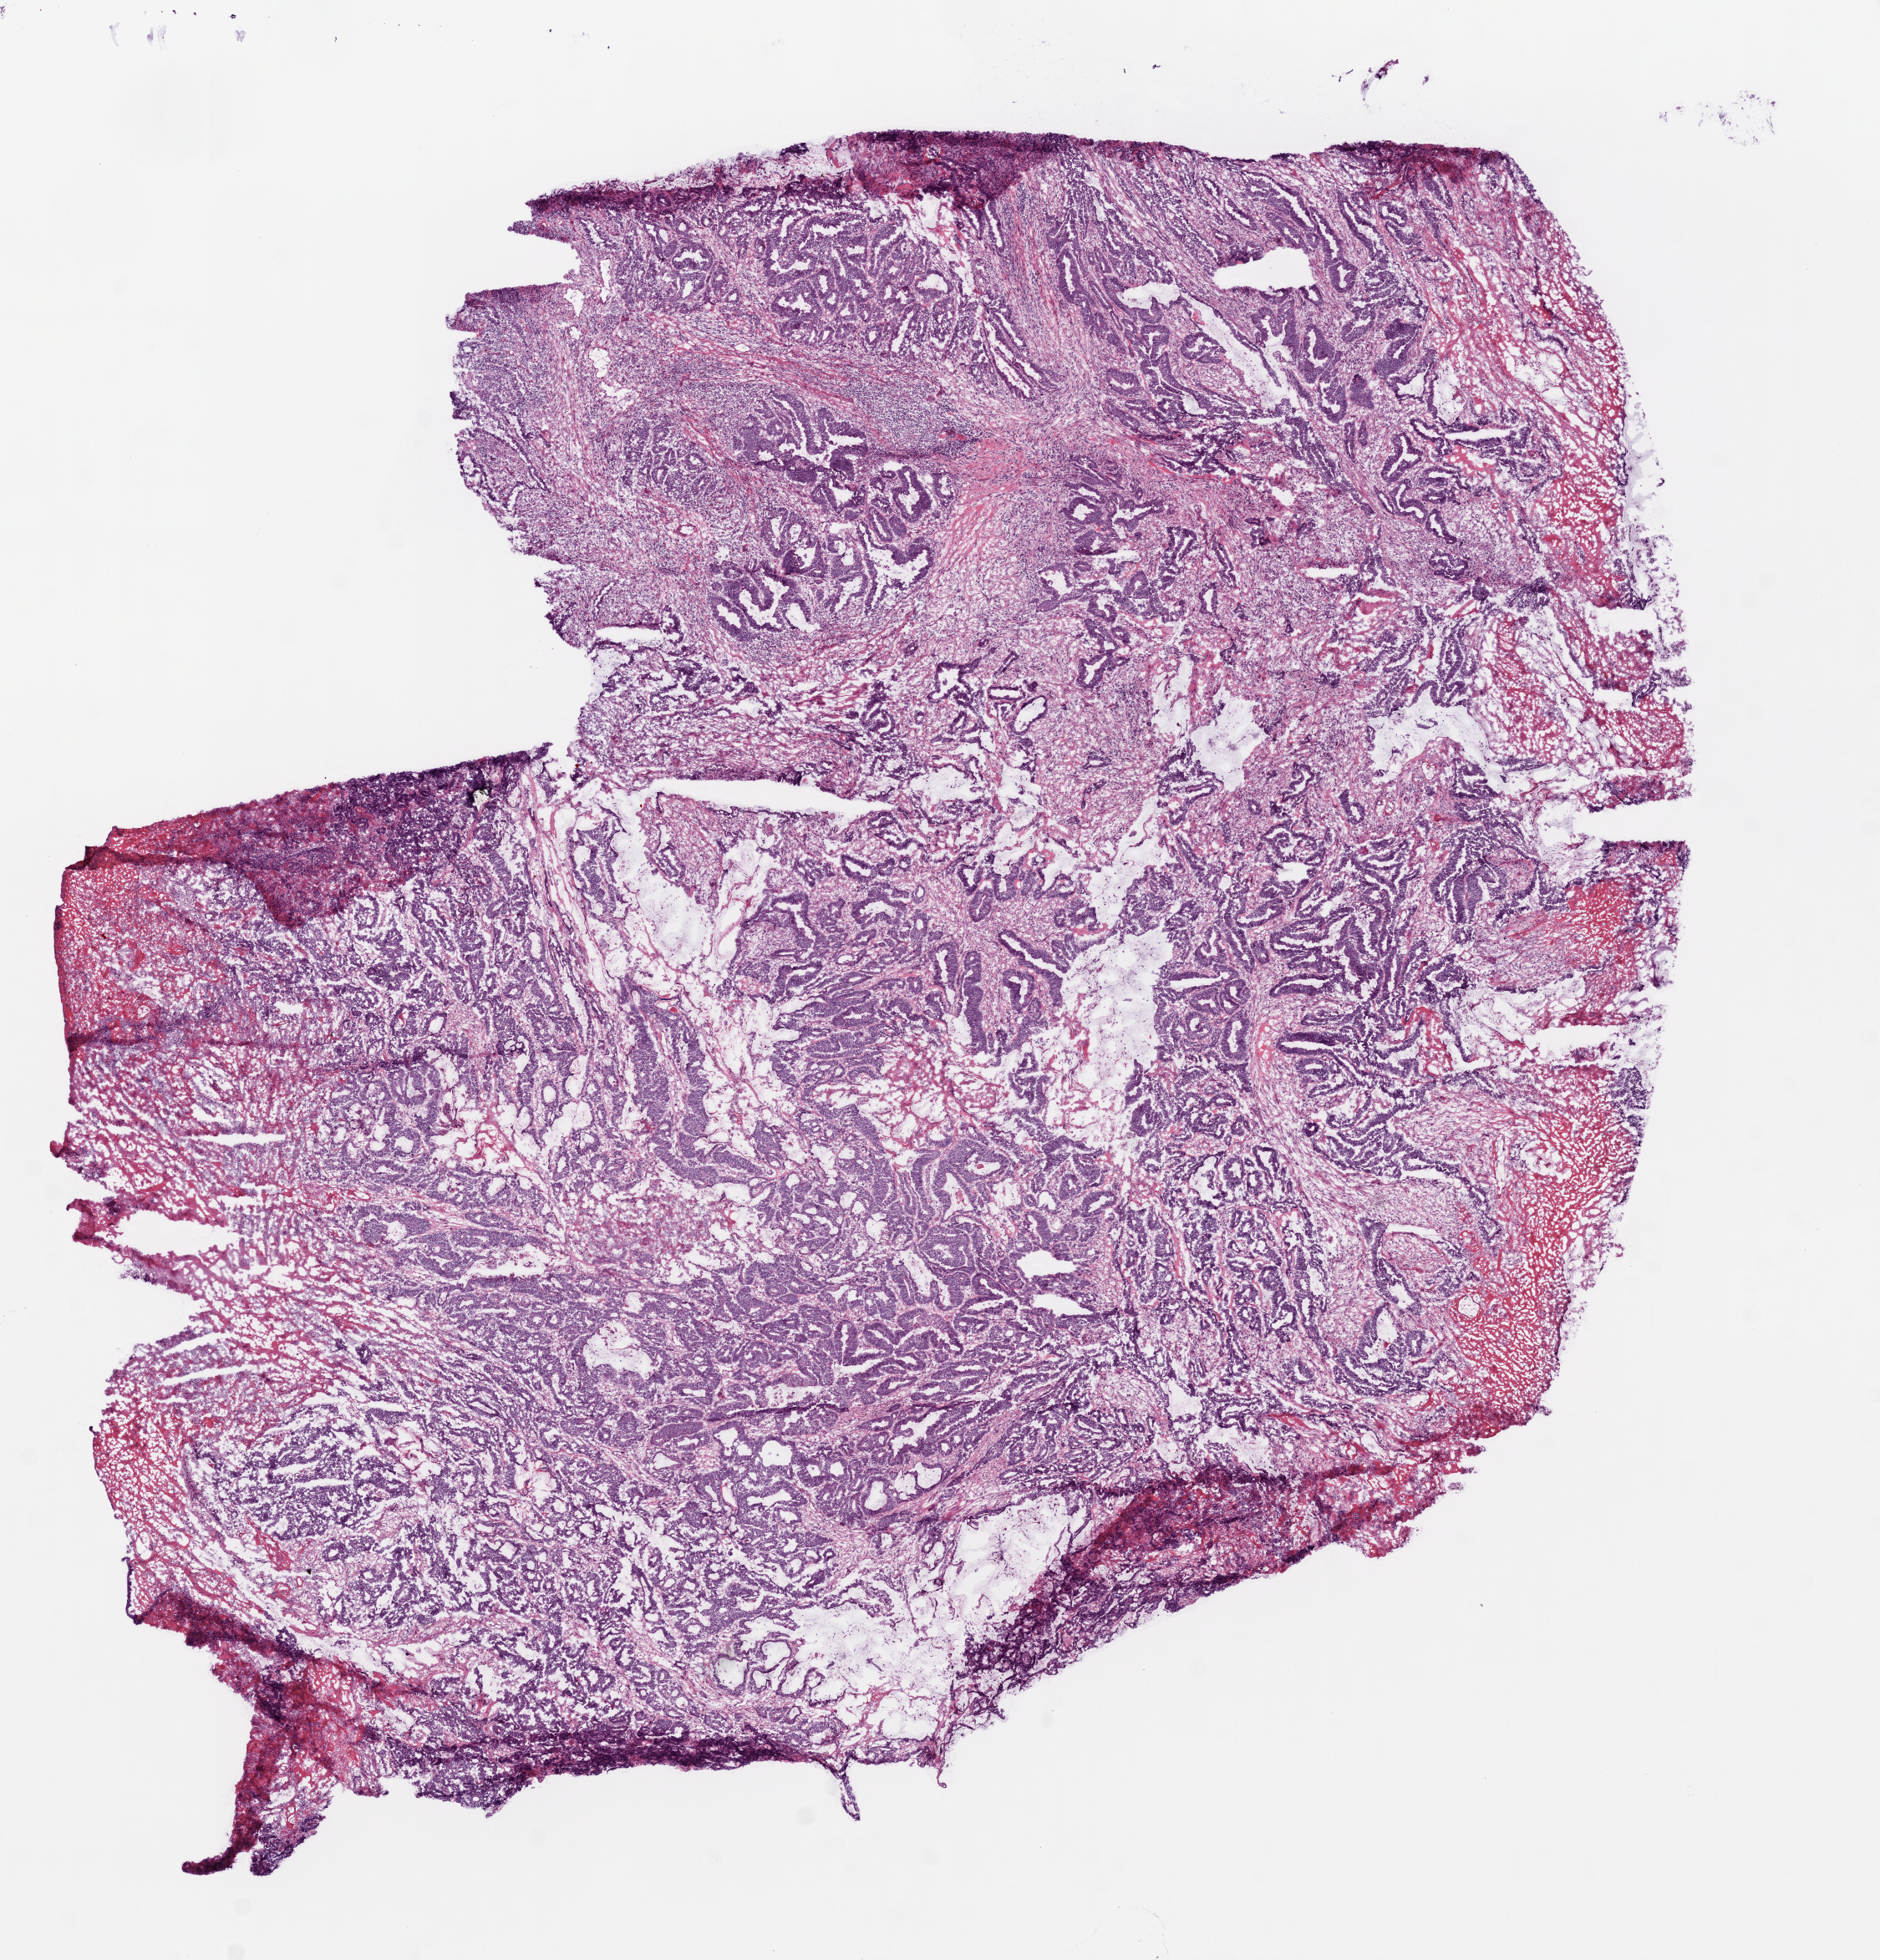
Hematoxylin and eosin (H&E) stained whole-slide image — low-resolution overview of the scanned area, about 9.0 x 9.4 mm (slide scanned at 20x); frozen section; primary tumour sample from the colon. Patient: female, age at initial diagnosis 60 years. Slide review estimates, as recorded: tumour cells 77%, tumour nuclei 75%, normal cells 5%, stromal cells 15%, necrosis 3%.
- AJCC pathologic stage: IIB (6th edition)
- histologic diagnosis: Mucinous adenocarcinoma
- TNM: T4 N0 M0